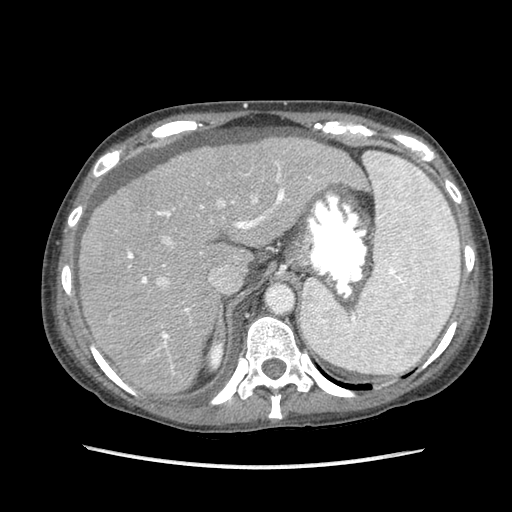
Contrast-enhanced abdominal CT (liver protocol), one axial slice; position 64 of 87 along the scan axis; reconstruction kernel STANDARD; soft-tissue window (W 400 / L 40 HU); 2.5 mm slice thickness; 512 × 512 image matrix. Case-level facts recorded for this patient, not image findings: diagnosis: hepatocellular carcinoma (patient treated with transarterial chemoembolisation; whether this scan precedes or follows treatment is not stated here); TNM stage (as recorded): Stage-IIIB; Child-Pugh class: A; tumour differentiation: no biopsy; tumour nodularity: uninodular.
Structures marked on this image (semi-automatic segmentation, software-assisted and operator-edited):
- abdominal aorta: bounding box <268,286,293,313> (left, top, right, bottom; pixels)
- liver parenchyma outside the tumour (the mass and vessels are separate outlines, so this box may not span the whole liver): <78,136,366,394>
- liver vessels: <127,162,351,374>